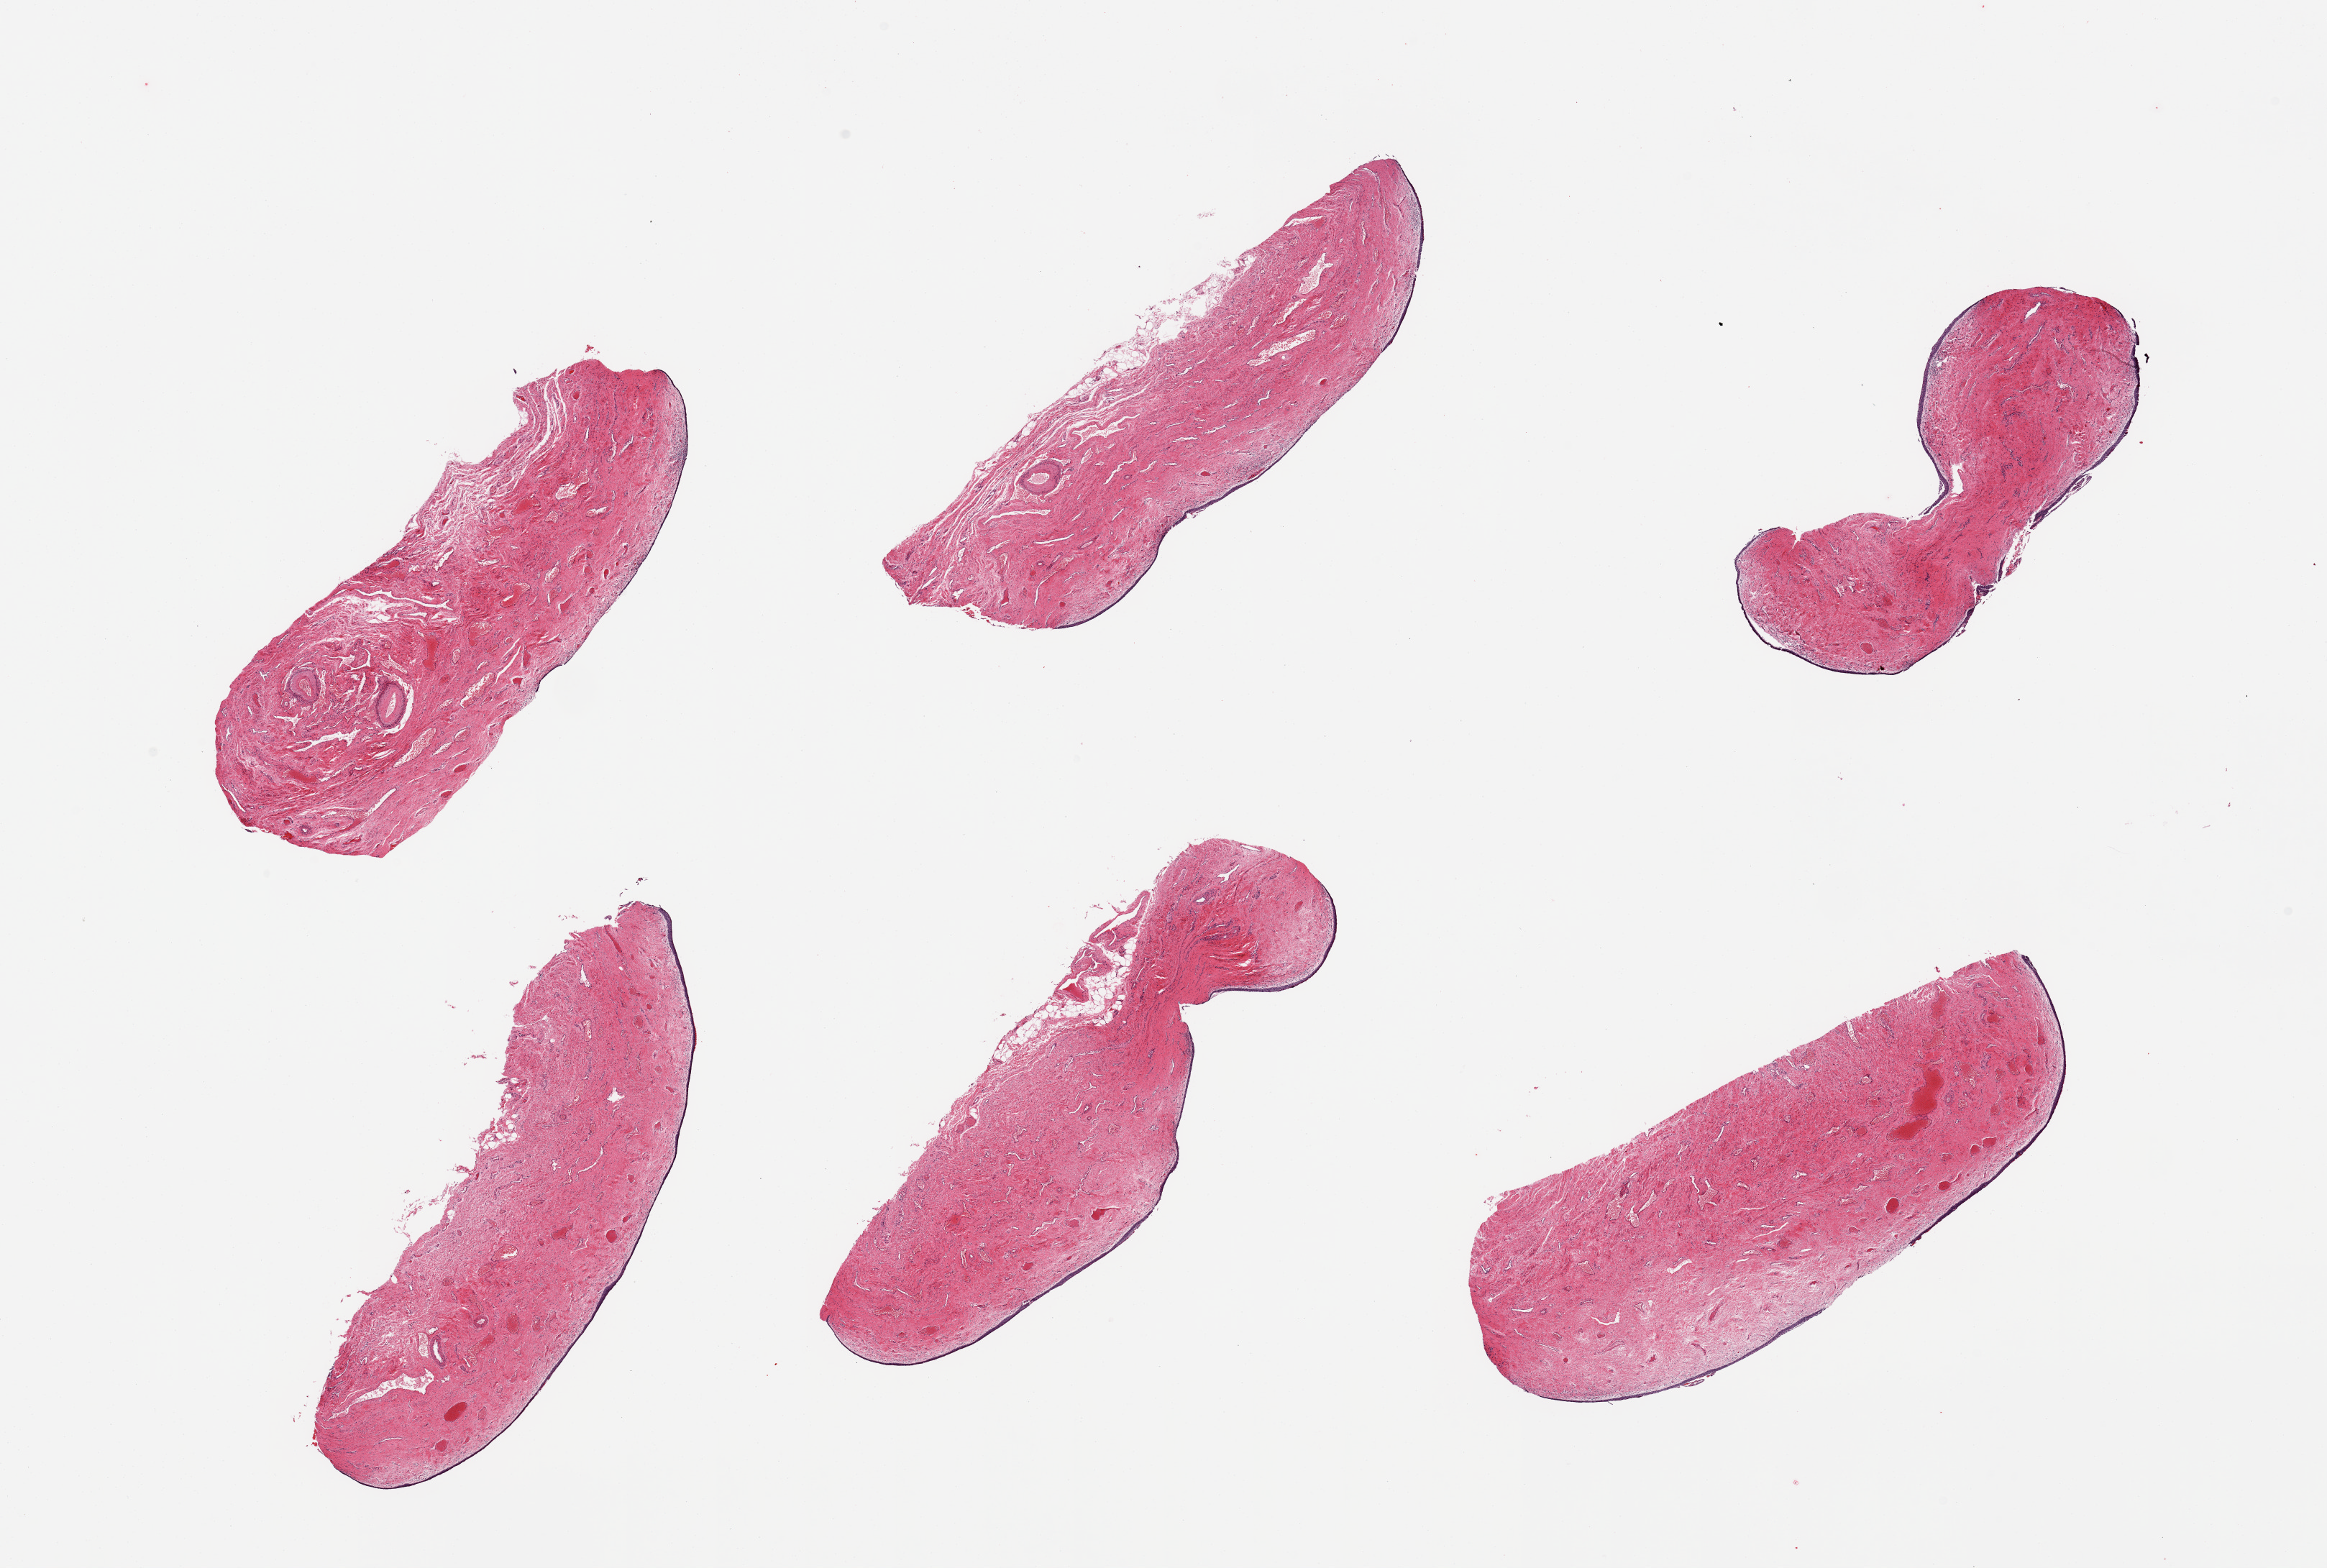
Digitized H&E-stained section — low-resolution overview of the scanned area, about 25.6 x 17.3 mm, PAXgene-fixed paraffin-embedded (PFPE) section, sampled site (target tissue): vagina, donor tissue sample. Donor sex: female.
* pathologist's review note for this sample: 6 pieces; thin atrophic epithelium